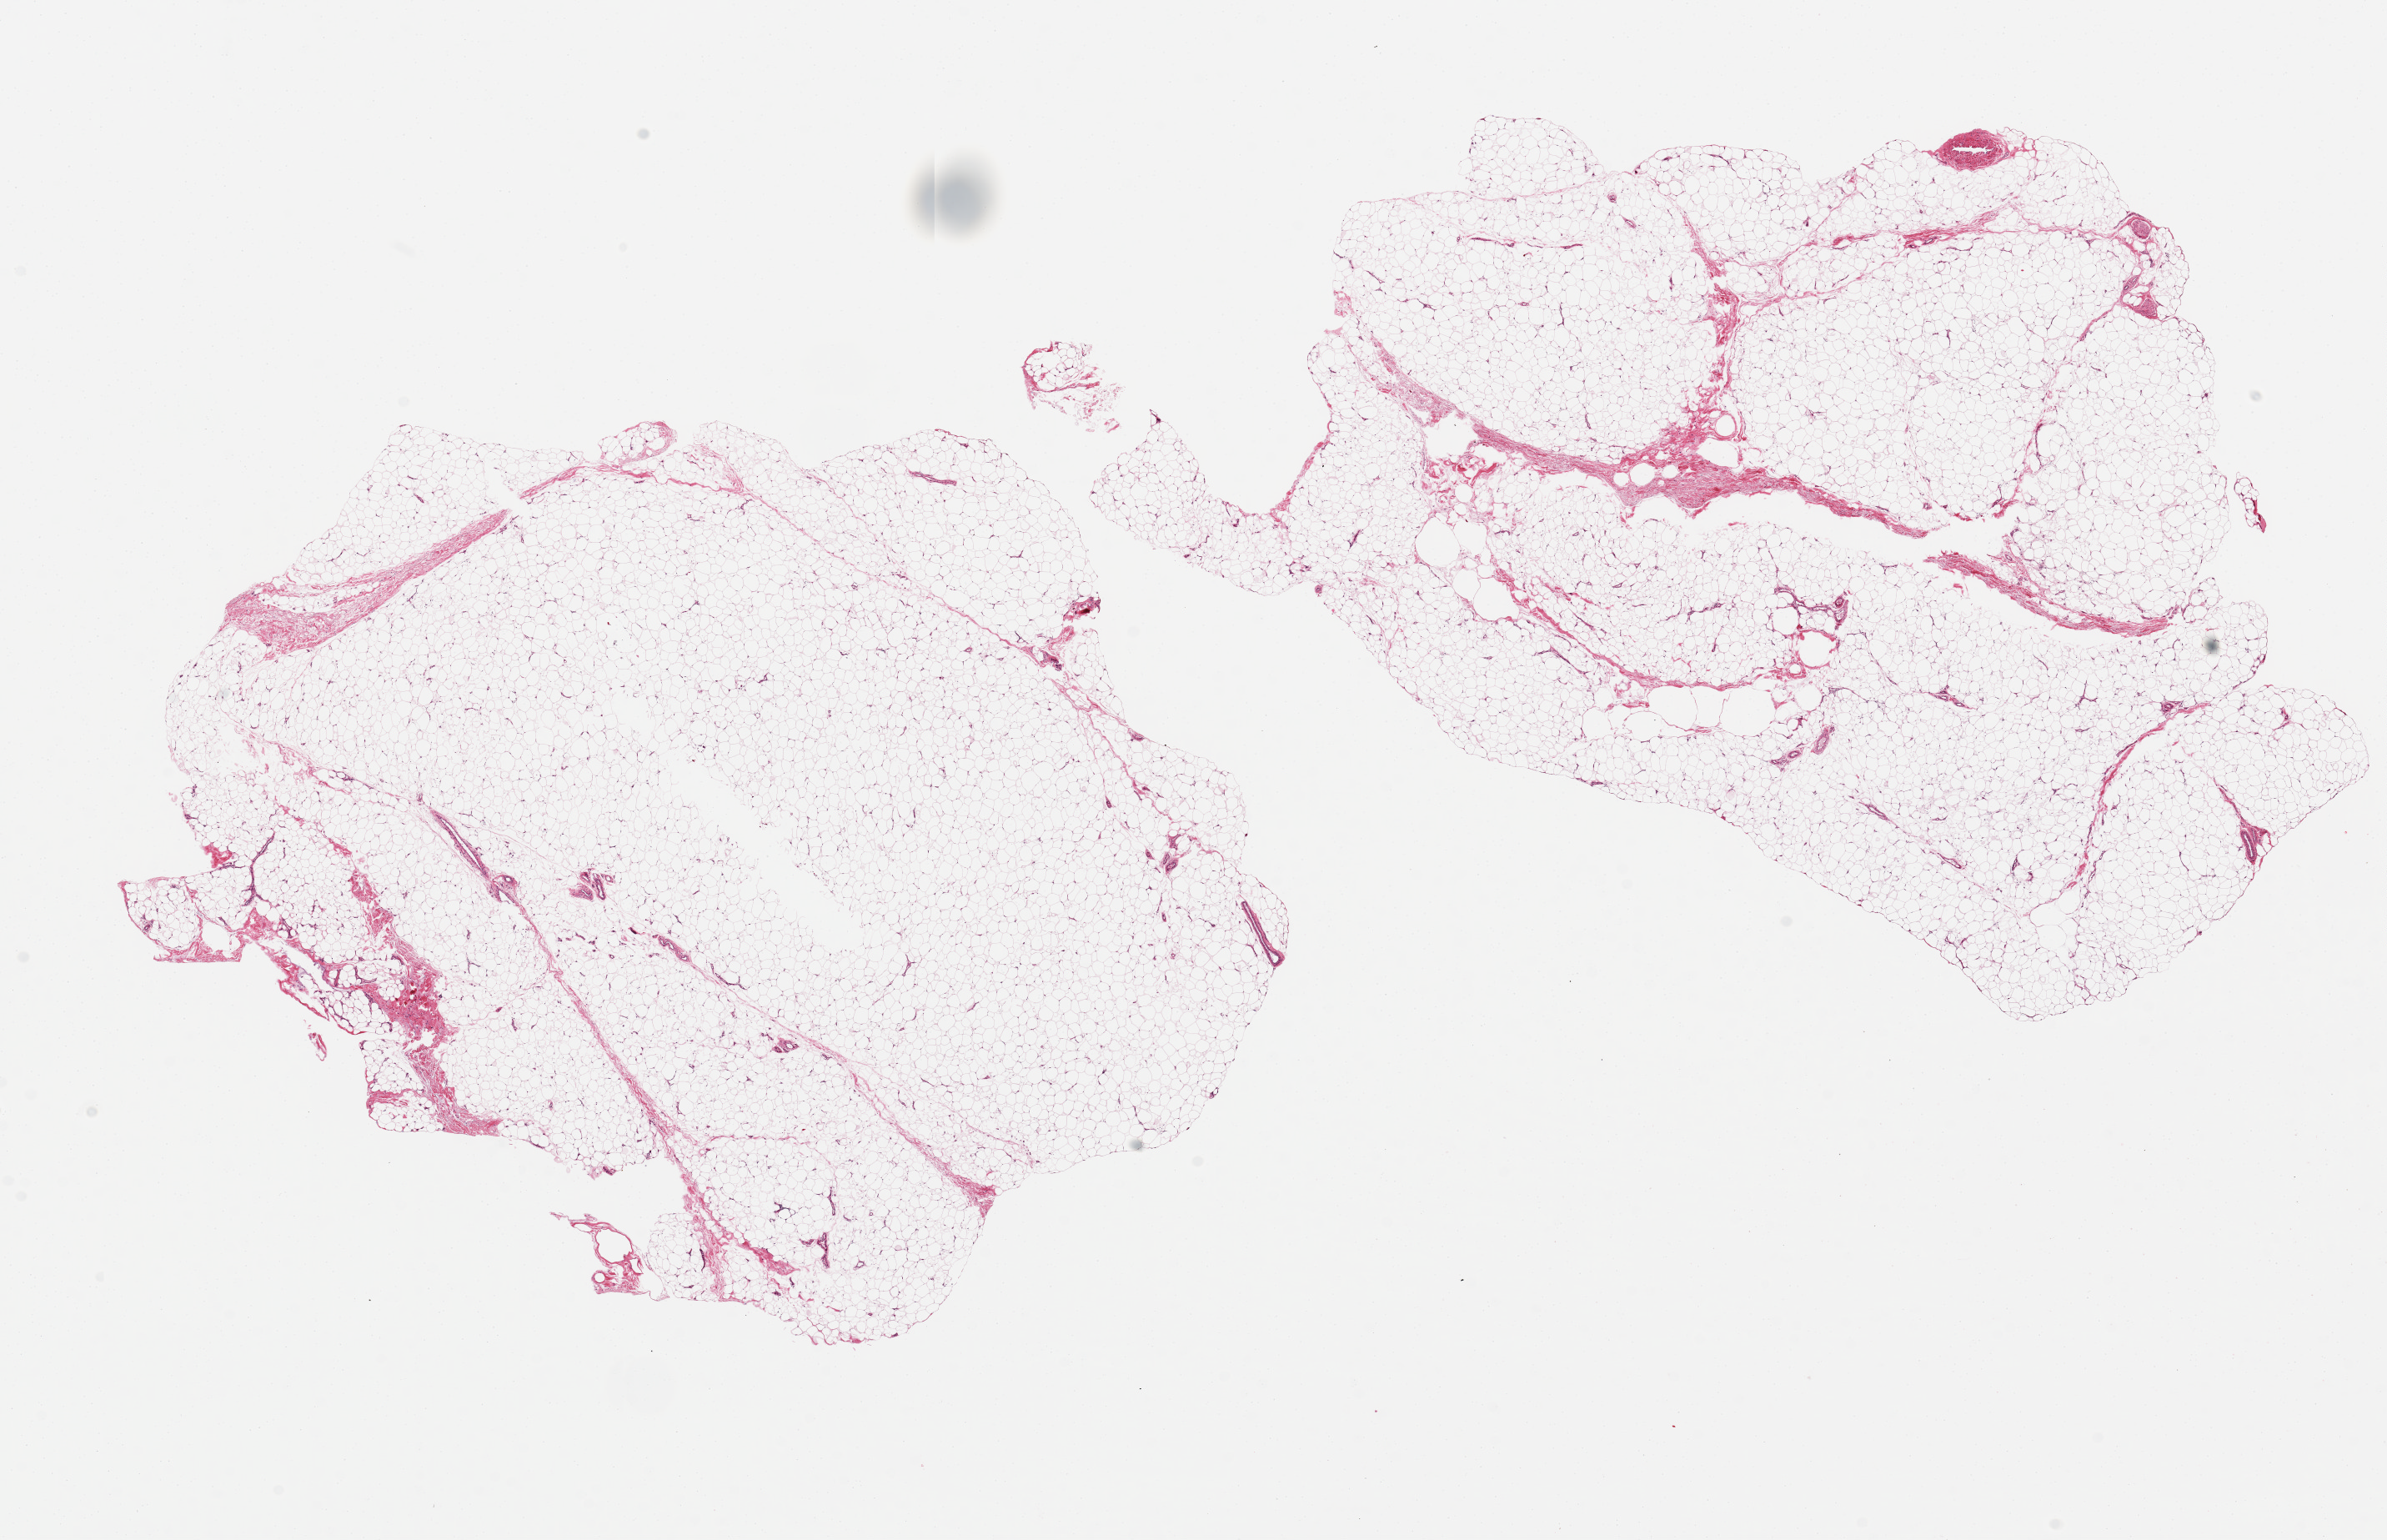
Haematoxylin and eosin whole-slide image — whole scanned area (about 22.6 x 14.6 mm, slide scanned at 20x) shown as a low-resolution overview, PAXgene-fixed, paraffin-embedded tissue, target tissue: adipose tissue, donor tissue sample.
Review note (as recorded): 2 aliquots, ~9x7mm.